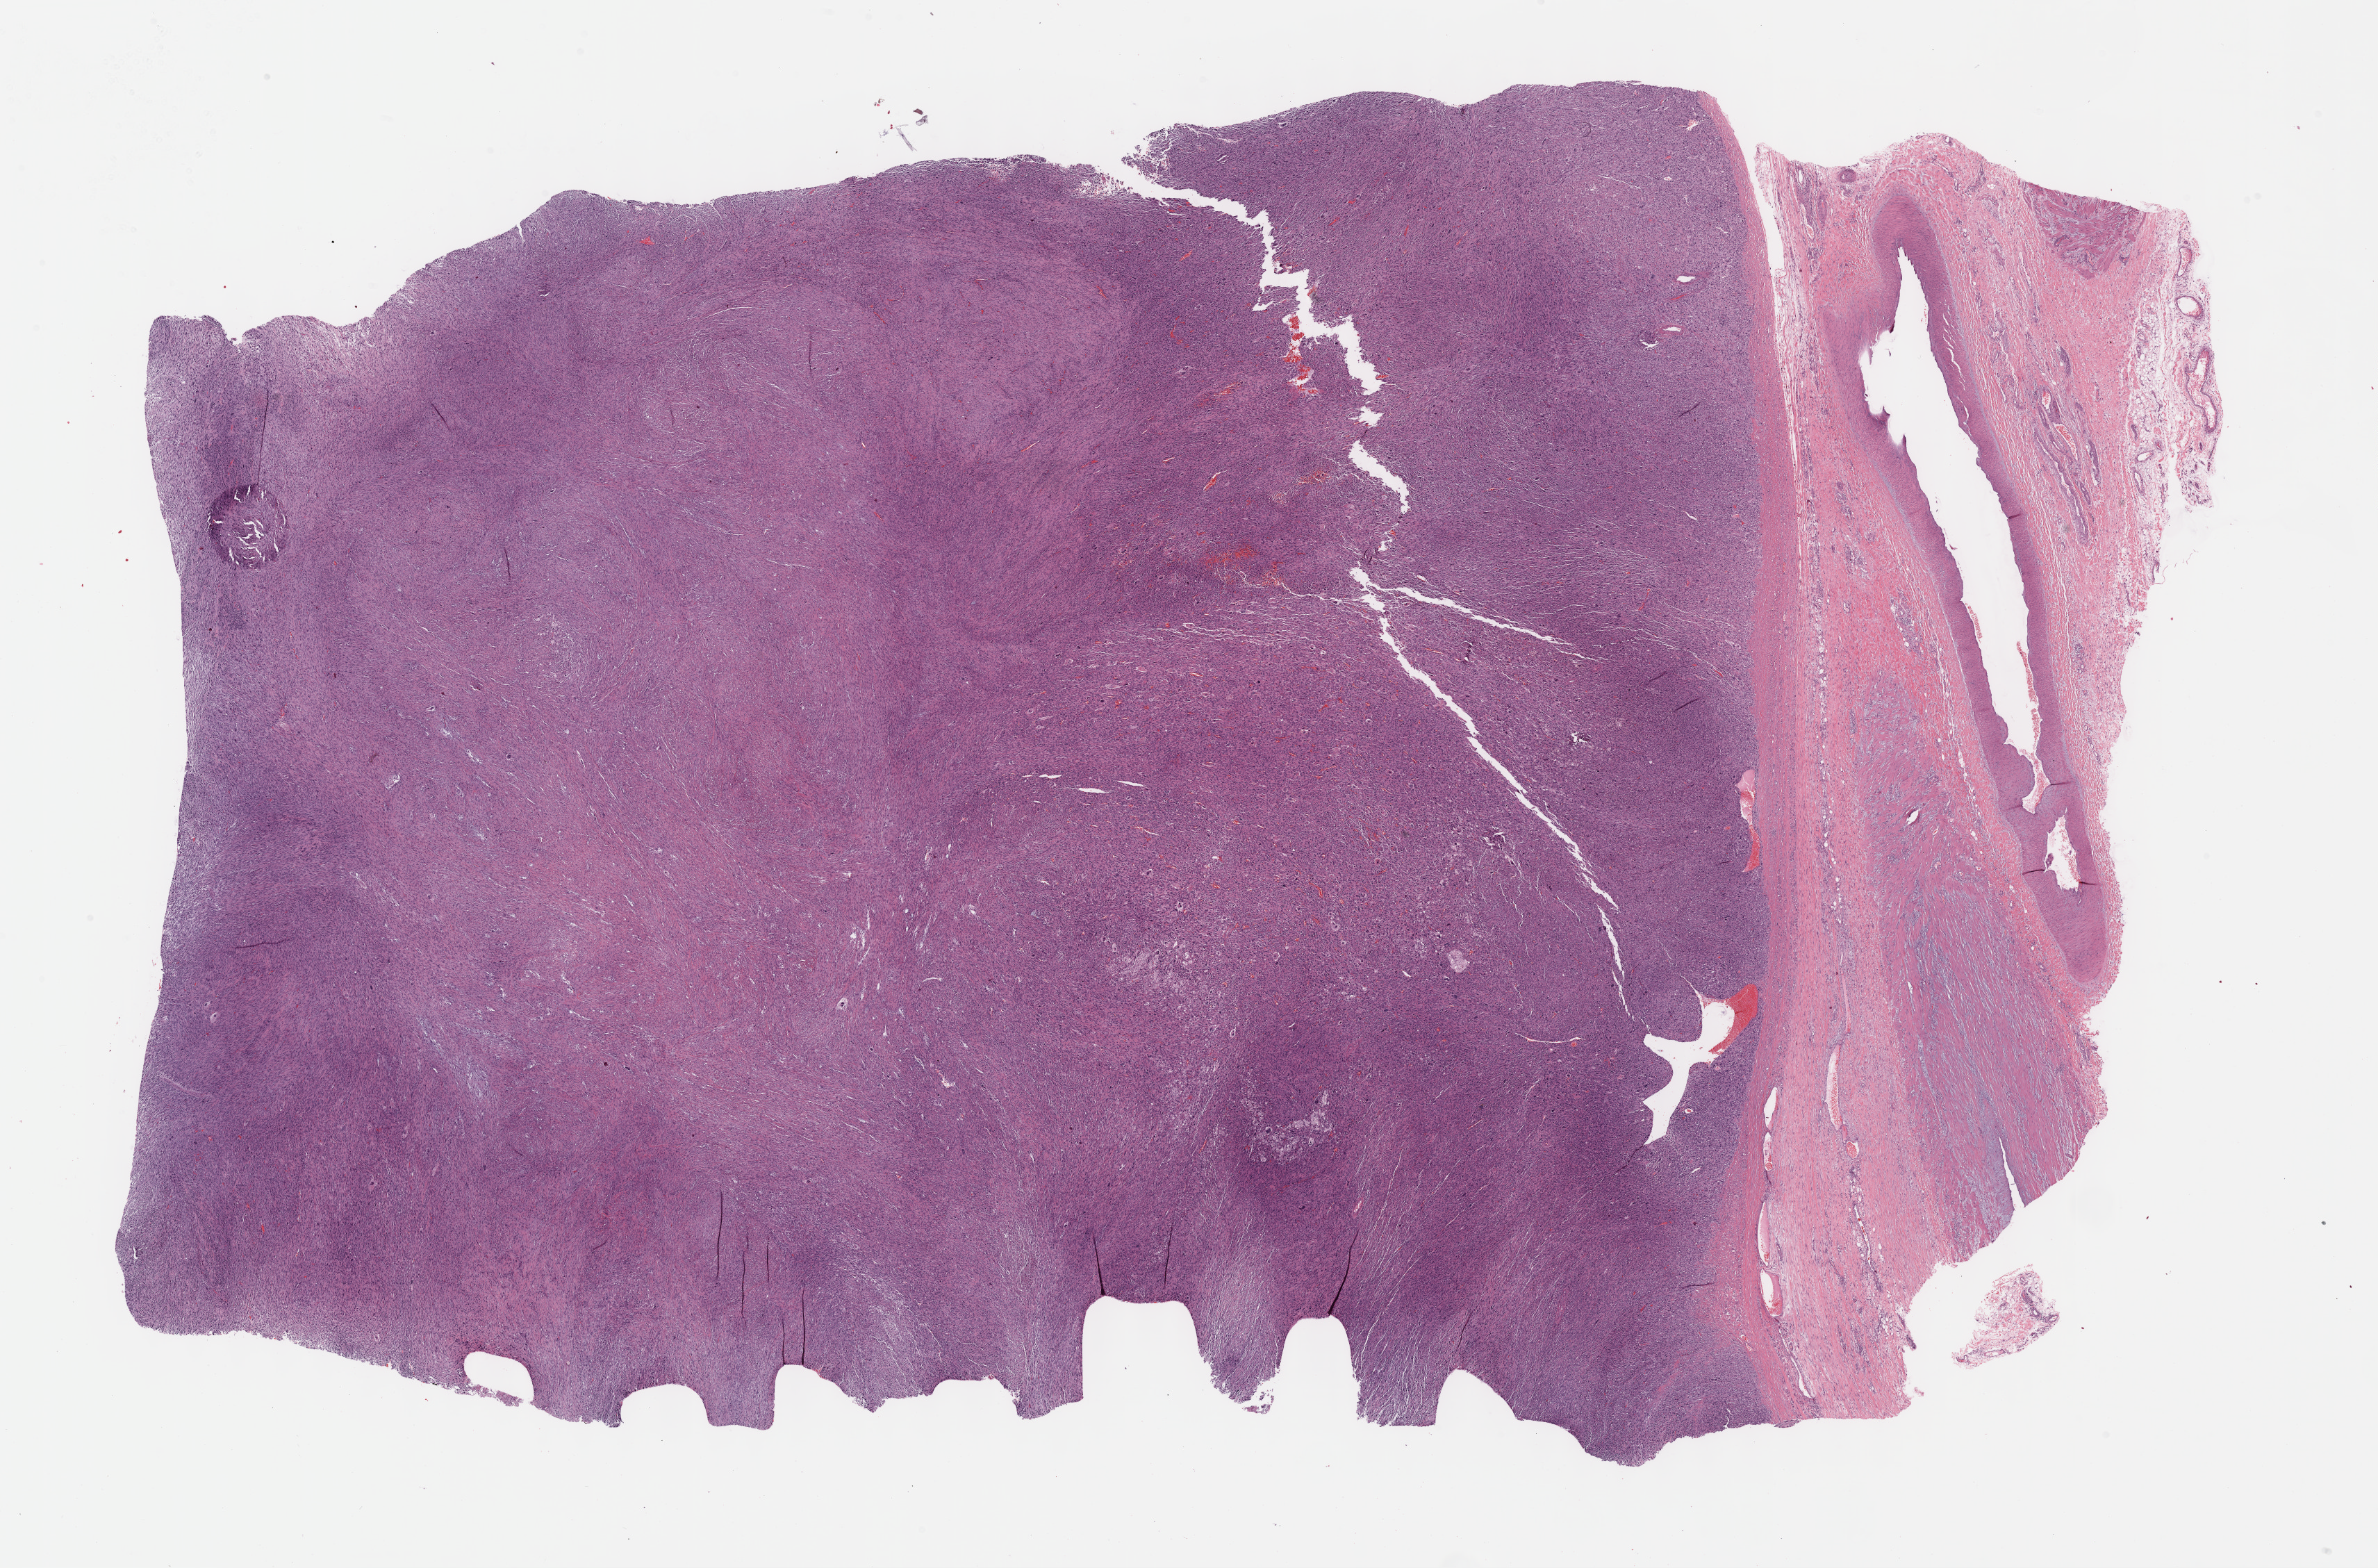
Digitized Hematoxylin and eosin (H&E) stained tissue section (whole slide) — a low-resolution overview of the entire scanned area, about 27.7 x 18.3 mm (acquisition: 40x scan); FFPE section; sample: primary tumour, connective, subcutaneous and other soft tissues. Patient: male, age at initial diagnosis 79 years.
Pathologic diagnosis: Malignant fibrous histiocytoma (connective, subcutaneous and other soft tissues of lower limb and hip).